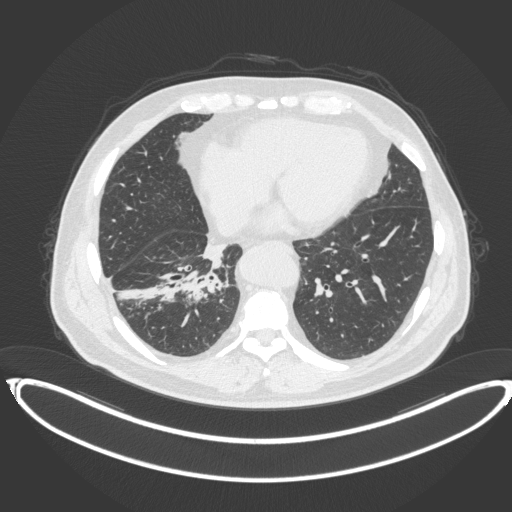
Chest CT, one axial slice; slice 142 of 383 in the series (ordered by position); reconstruction kernel B31f; 120 kVp; lung window (W 1500 / L -600 HU); 1 mm slice thickness; 512 × 512 image matrix, field of view 448 × 448 mm. Male patient, age 61 years. Case-level facts recorded for this patient, not image findings: clinical TNM (as recorded): T1b N1 M0.
Structures marked on this image (rectangle marked by the reading radiologist):
- lung tumour (recorded histology: squamous cell carcinoma): bounding box <176,268,224,303> (left, top, right, bottom; pixels)